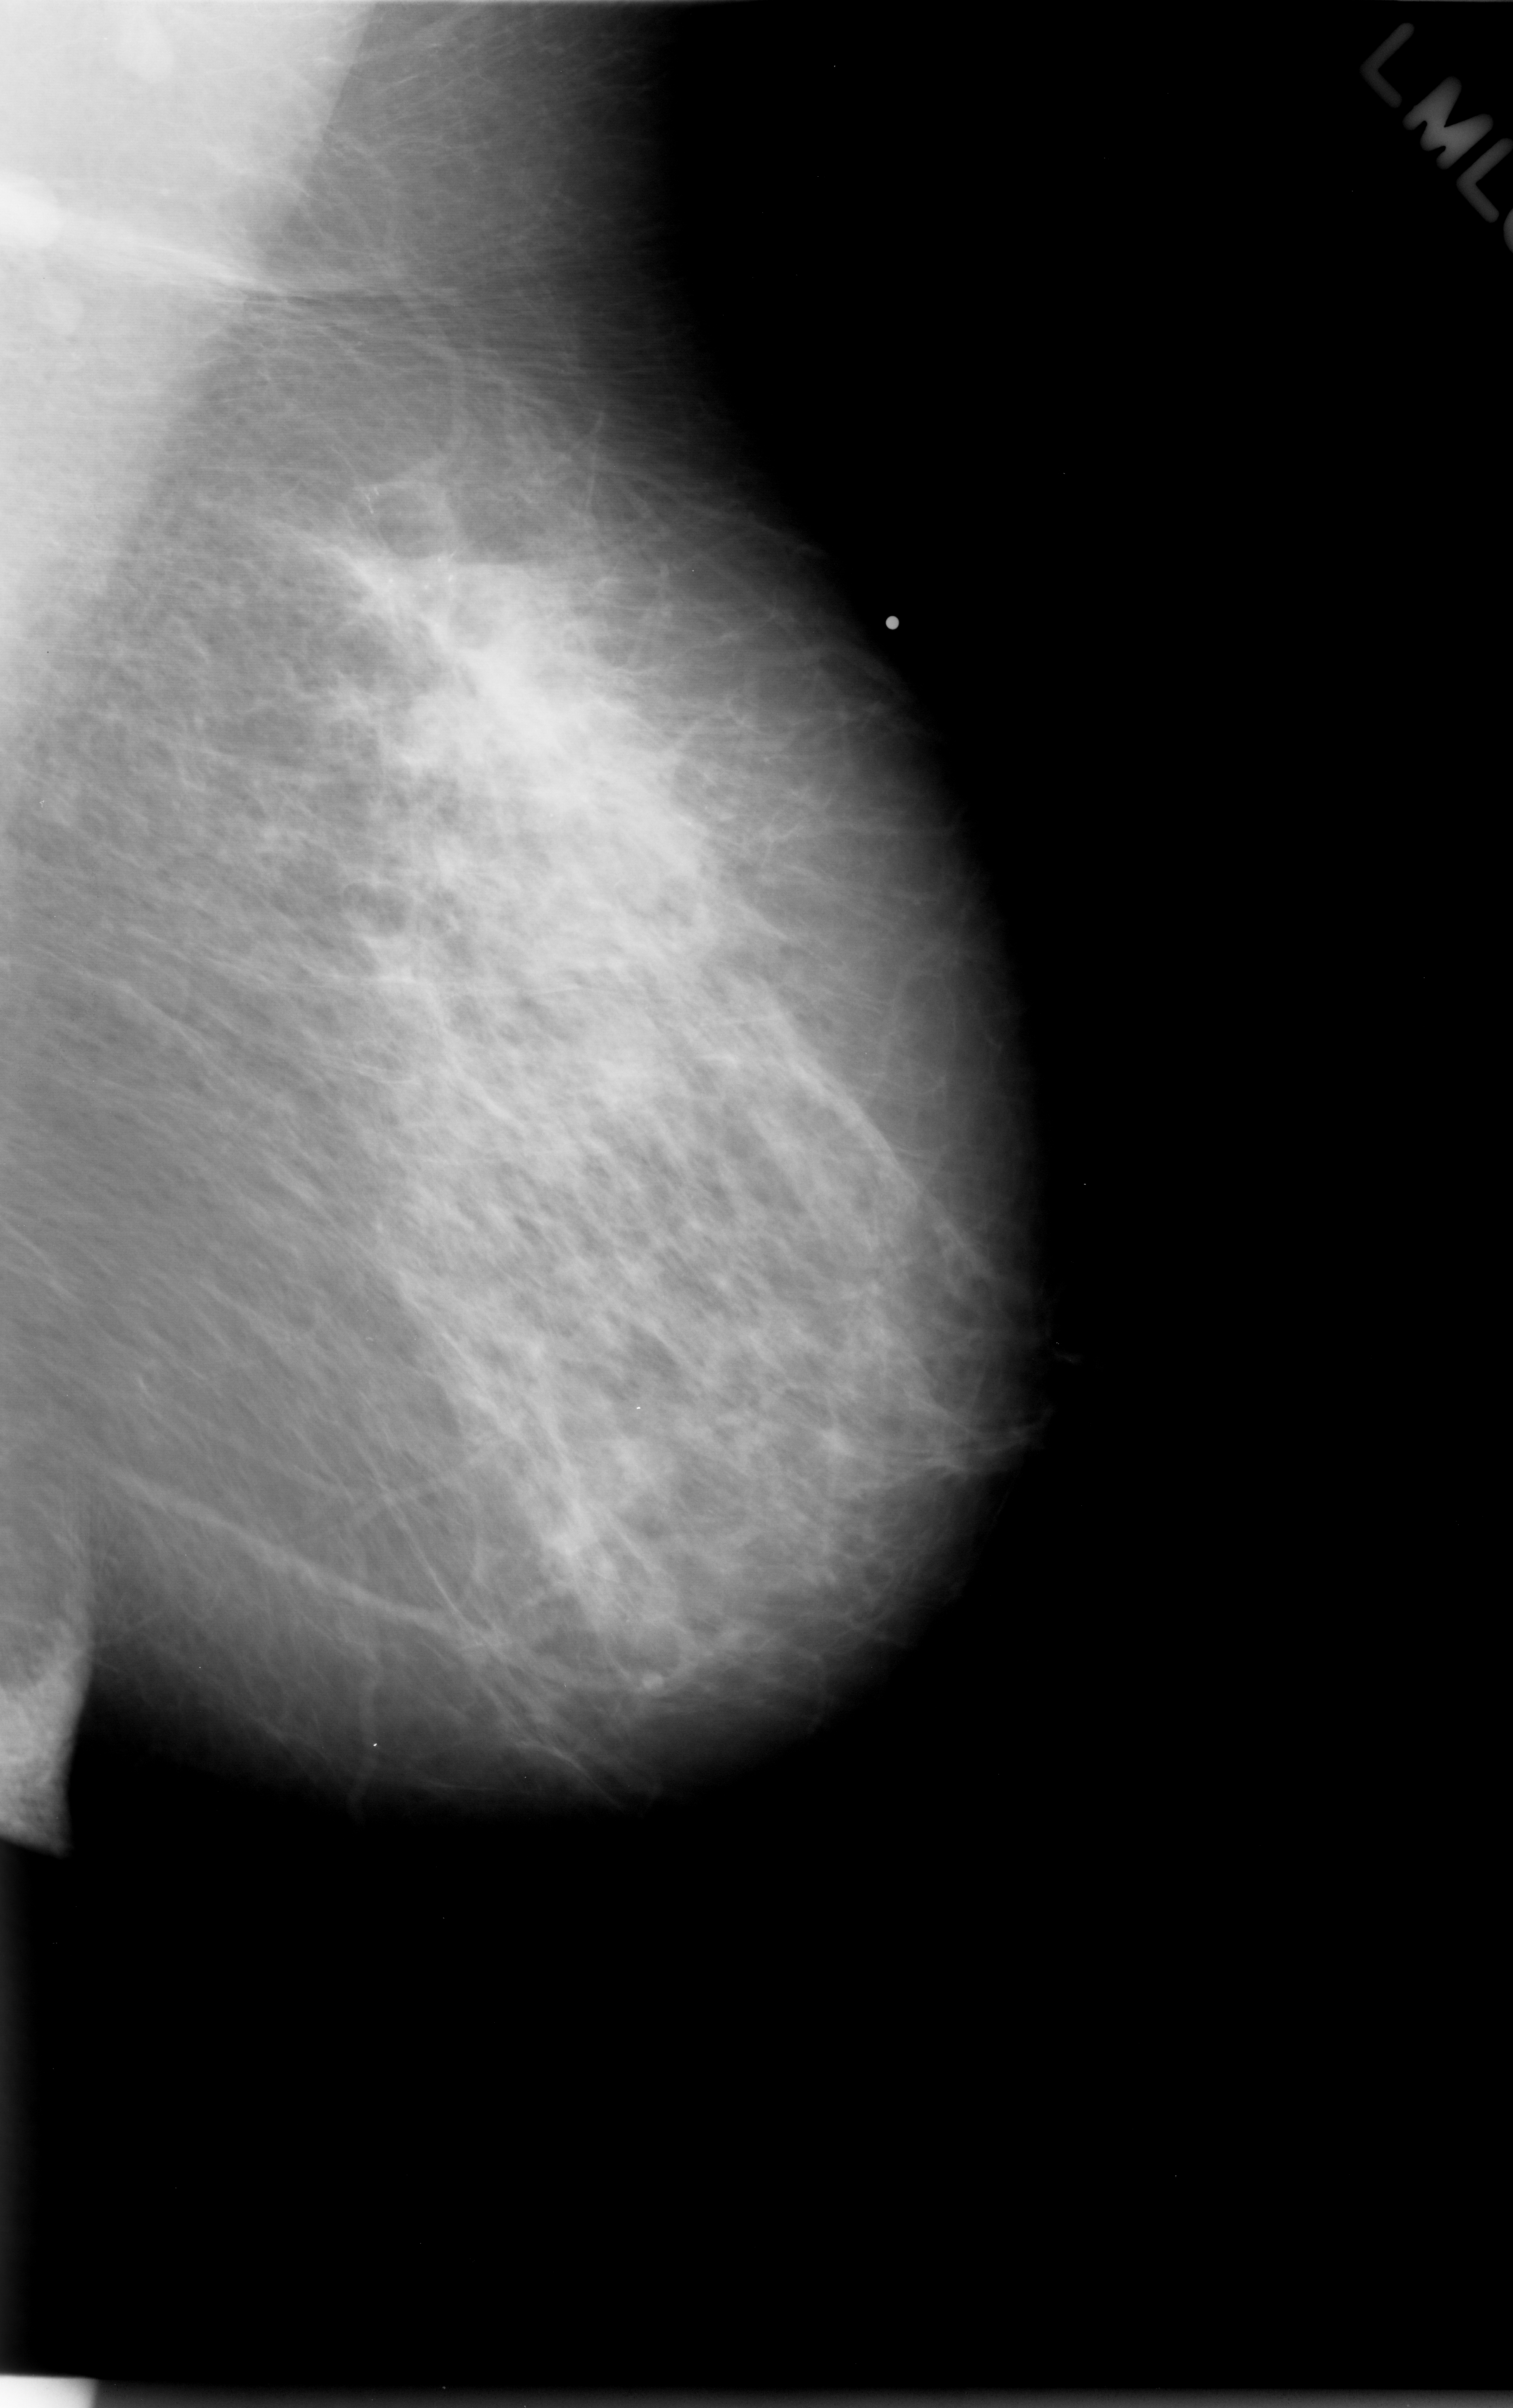
Mammogram (digitized film), left breast, mediolateral oblique (MLO) view.
Radiologist-marked abnormalities on this image: calcifications, morphology pleomorphic, distribution regional; BI-RADS assessment category 4; subtlety rating 2 on a 1 (subtle) to 5 (obvious) scale; pathology result (as recorded, not read from the image): malignant.